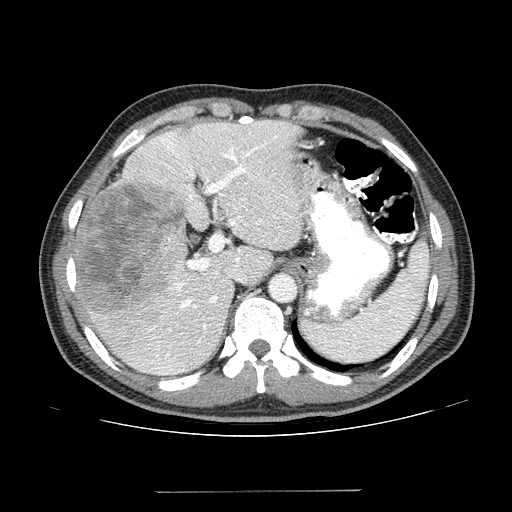
Contrast-enhanced abdominal CT (liver protocol), one axial slice. Position 99 of 131 along the scan axis. Reconstruction kernel STANDARD. One of 2 acquisitions stored at this slice position. Soft-tissue window (W 400 / L 40 HU). 2.5 mm slice thickness. 512 × 512 image matrix, field of view 380 × 380 mm. From the clinical record (not read from this slice): diagnosis: hepatocellular carcinoma (patient treated with transarterial chemoembolisation; whether this scan precedes or follows treatment is not stated here); TNM stage (as recorded): Stage-I; Child-Pugh class: A; tumour differentiation: poorly differentiated; tumour nodularity: uninodular.
Annotated regions visible in this slice (semi-automatically segmented with operator editing):
- liver parenchyma outside the tumour (the mass and vessels are separate outlines, so this box may not span the whole liver): box from (x=72, y=120) to (x=302, y=376) px
- mass: (x=77, y=182)–(x=189, y=317)
- liver vessels: (x=140, y=125)–(x=294, y=375)